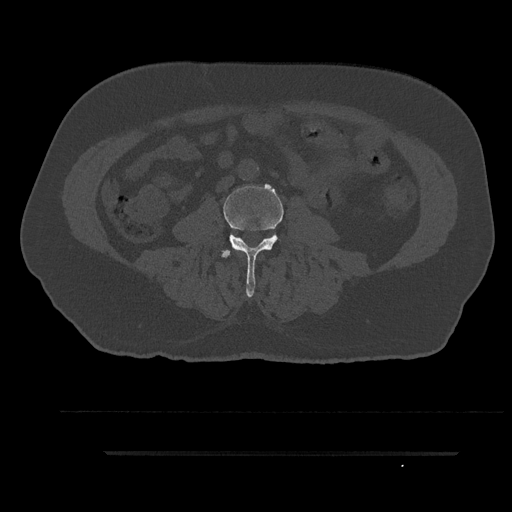
CT including the spine, one axial slice. Slice 33 of 797 in the series (ordered by position). Reconstruction kernel Br40s/3. Bone window (W 1800 / L 400 HU). 0.5 mm slice thickness. 512 × 512 image matrix, field of view 432 × 432 mm. Patient: male, 63 years. Case-level facts recorded for this patient, not image findings: primary cancer: renal; vertebrae with lytic lesions (as recorded): T8.
Outlined on this slice (semi-automatic segmentation, software-assisted and operator-edited):
- L3 vertebra: bounding box (x1, y1, x2, y2) in pixels: (221, 185, 284, 297)